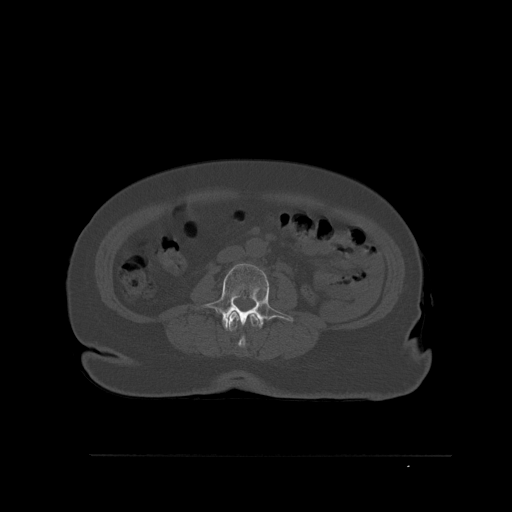
CT including the spine, one axial slice. Position 228 of 527 along the scan axis. Bone window (W 1800 / L 400 HU). 1.5 mm slice thickness. 512 × 512 image matrix, field of view 470 × 470 mm. Female patient, age 73 years. From the clinical record (not read from this slice): primary cancer: breast.
Structures marked on this image (semi-automatic segmentation, software-assisted and operator-edited):
- L2 vertebra: bounding box <228,312,259,348> (left, top, right, bottom; pixels)
- L3 vertebra: <197,263,294,331>